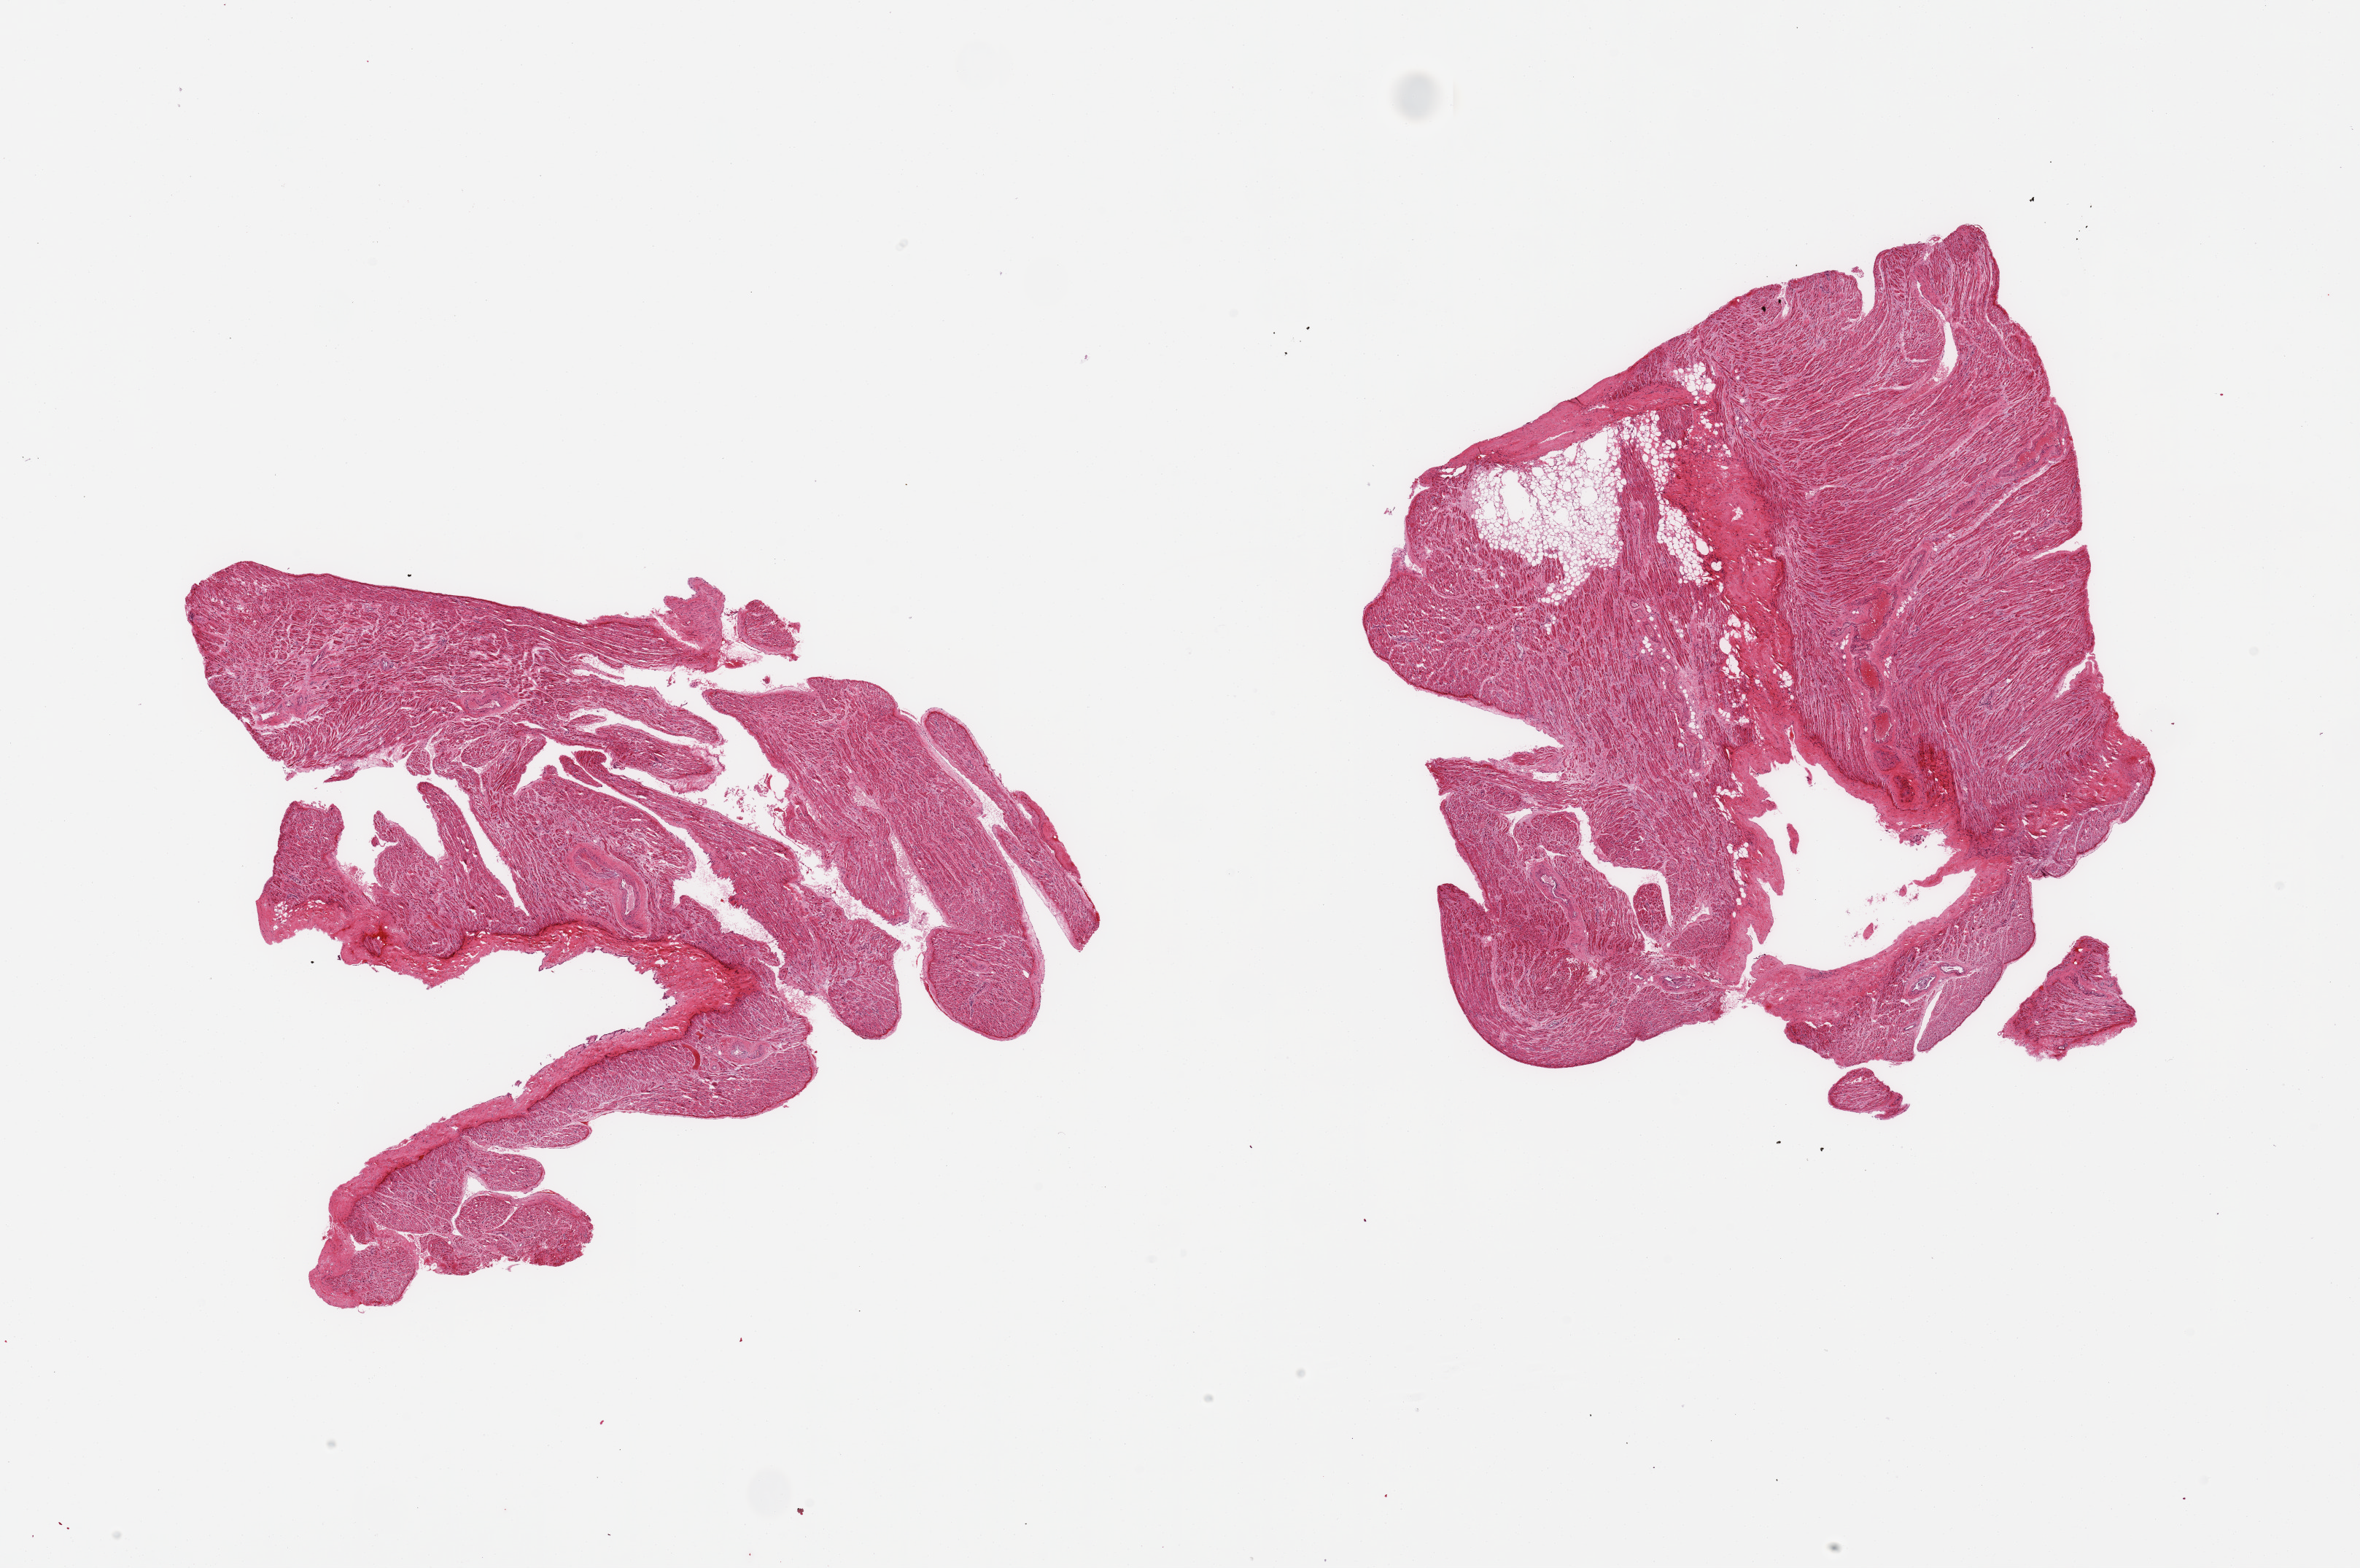
Digitized hematoxylin and eosin (H&E)-stained section — shown as a low-resolution overview of the whole scanned area (about 25.6 x 17.0 mm, acquisition: 20x scan). PAXgene-fixed, paraffin-embedded tissue. Section of auricular appendage (target tissue). Tissue donor sample. Donor: female.
* review note (as recorded): 2 pieces; 10% internal fat content